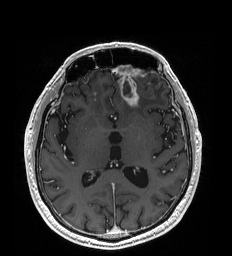
Brain MRI from a brain-tumour surgery series, one axial slice. Position 102 of 192 along the scan axis. T1-weighted post-contrast. 232 × 256 image matrix, field of view 227 × 250 mm. From the clinical record (not read from this slice): histopathology: Glioblastoma; WHO grade: 4; IDH mutation: no.
Outlined on this slice (outlined manually by an expert reader):
- tumour: box from (x=121, y=85) to (x=139, y=106) px